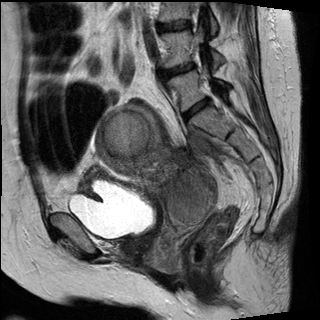
Pelvic MRI for cervical cancer, one sagittal slice. Slice 13 of 30 in the series (ordered by position). T2-weighted. 1.5 T. TE 89 ms, TR 2930 ms. 320 × 320 image matrix, field of view 260 × 260 mm. Female patient, age 62 years.
Structures marked on this image (outlined manually by an expert reader):
- uterus and cervix: bounding box (x1, y1, x2, y2) in pixels: (97, 102, 216, 227)